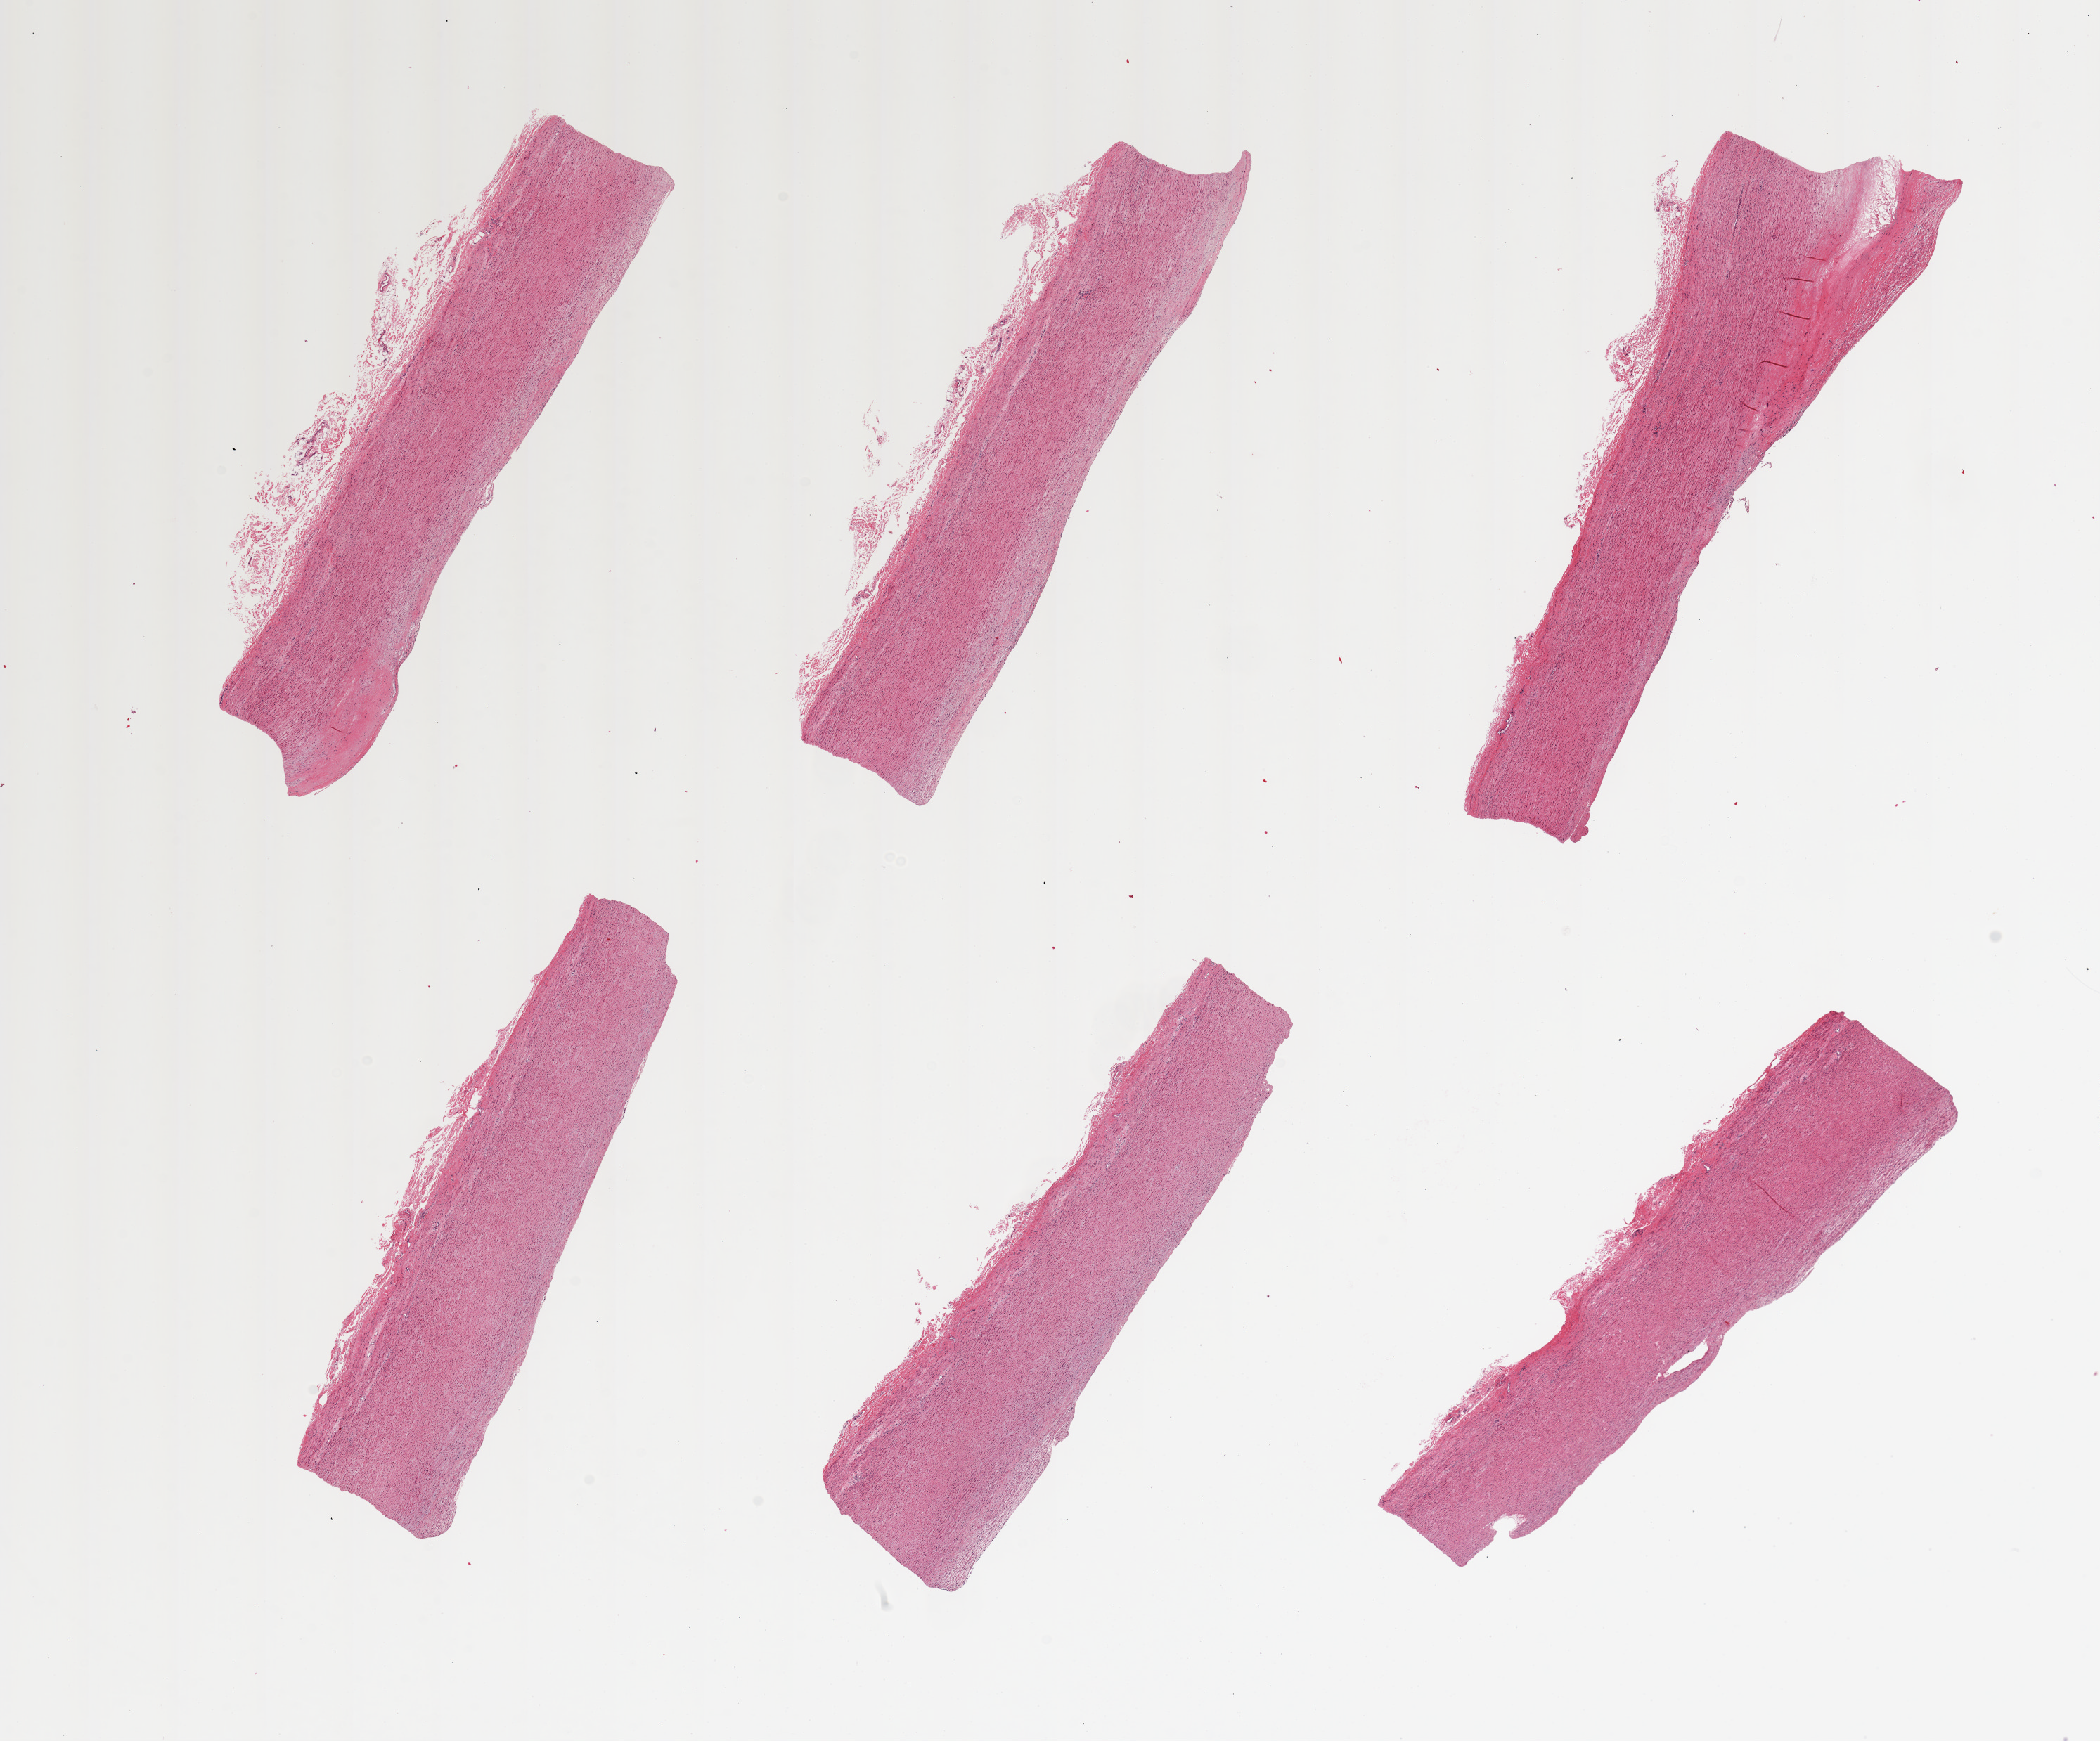
Whole-slide image, H&E stain — shown as a low-resolution overview of the whole scanned area (about 23.6 x 19.6 mm, acquisition: 20x scan), PAXgene-fixed, paraffin-embedded tissue, section of aorta (target tissue), tissue donor sample. Donor: male.
Reviewer comment on this tissue sample: 6 pieces, atherosclerosis.